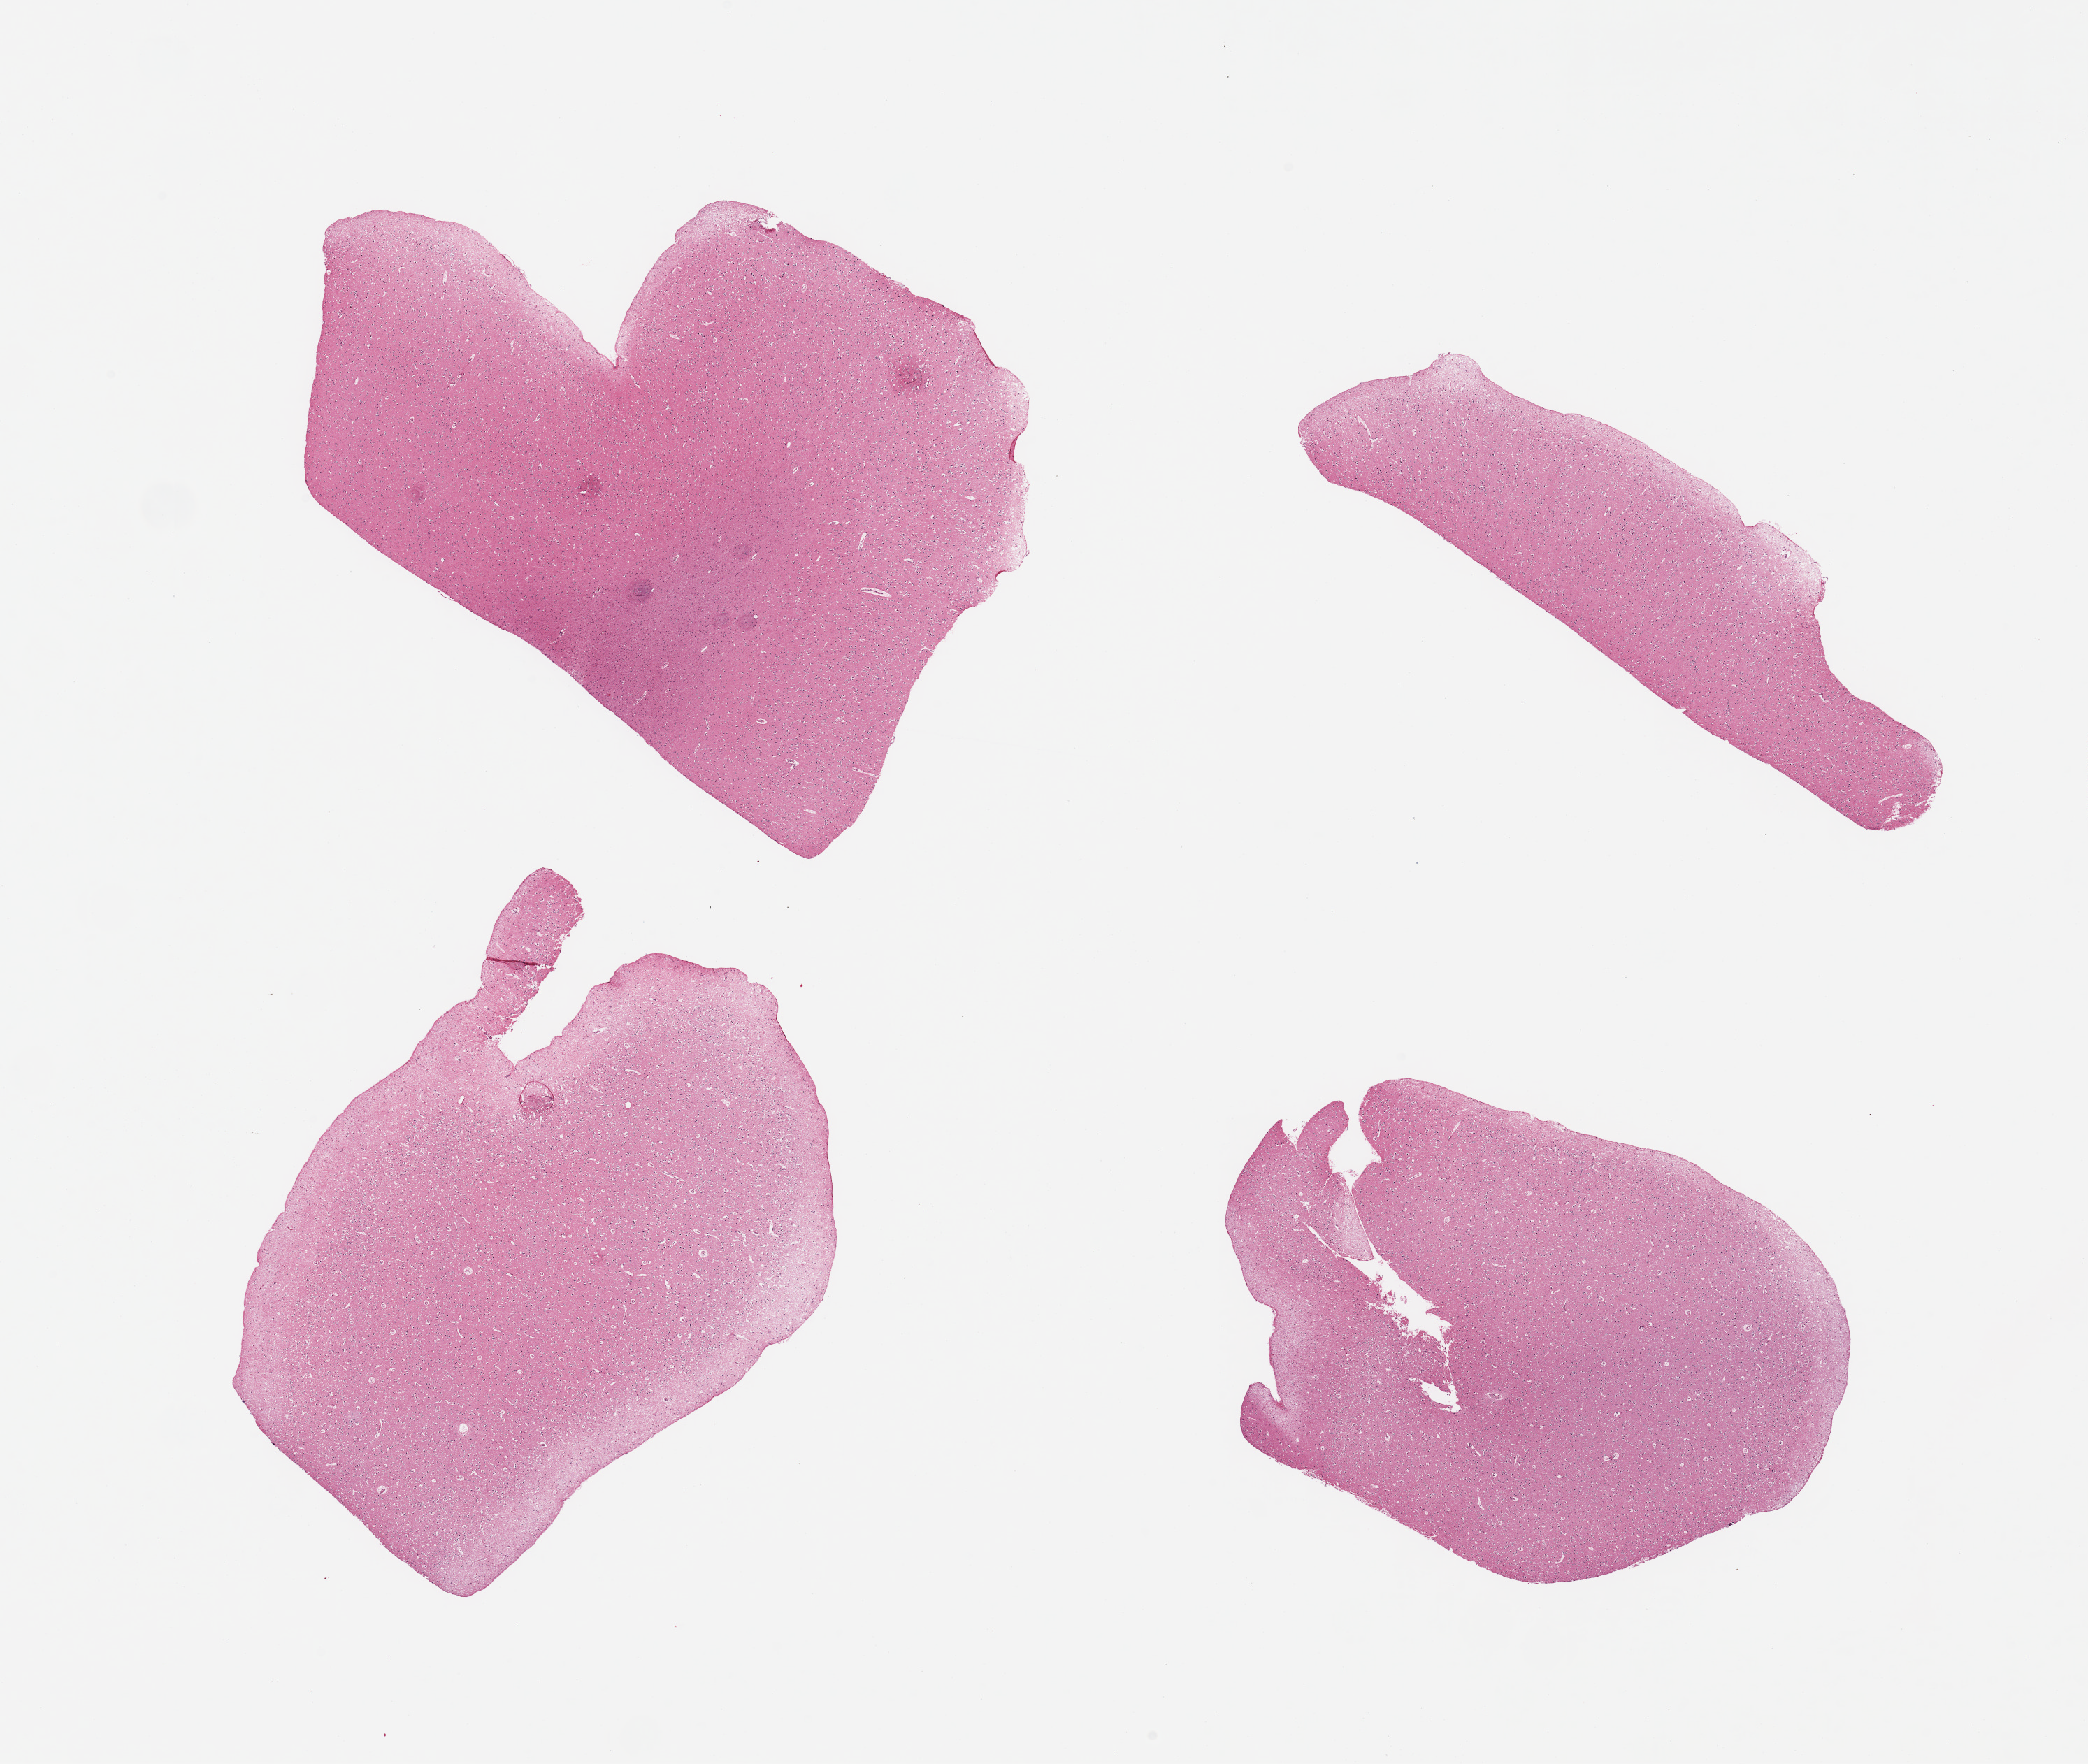
Digitized H&E-stained section, brightfield, a low-resolution overview of the entire scanned area, about 23.6 x 20.0 mm (from a 20x scan); PAXgene-fixed paraffin-embedded (PFPE) section; sampled site (target tissue): cerebral cortex; tissue donor sample. Donor: female.
- pathologist's review note for this sample: 4 pieces; cerebral cortex (not pituitary)